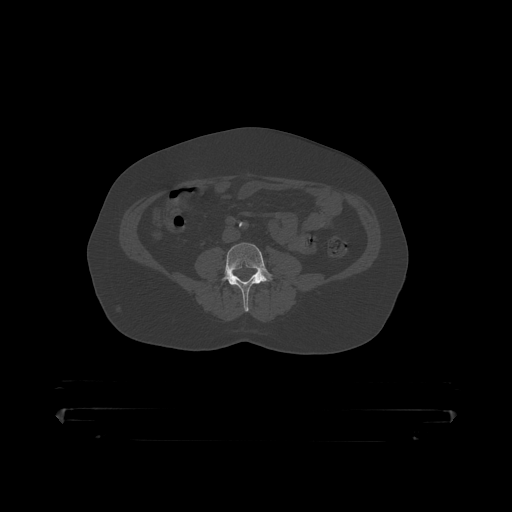
CT including the spine, one axial slice. Position 64 of 390 along the scan axis. Bone window (W 1800 / L 400 HU). 1.25 mm slice thickness. 512 × 512 image matrix, field of view 650 × 650 mm. Male patient, age 60 years. From the clinical record (not read from this slice): primary cancer: prostate.
Structures marked on this image (semi-automatically segmented with operator editing):
- L3 vertebra: bounding box [x1, y1, x2, y2] px = [234, 285, 237, 288]
- L4 vertebra: [219, 243, 277, 312]